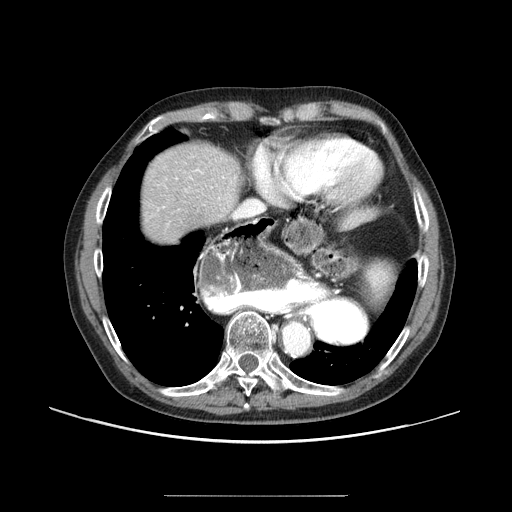
Contrast-enhanced abdominal CT (liver protocol), one axial slice. Position 77 of 91 along the scan axis. Reconstruction kernel STANDARD. 100 kVp. One of 2 acquisitions stored at this slice position. Soft-tissue window (W 400 / L 40 HU). 2.5 mm slice thickness. 512 × 512 image matrix, field of view 400 × 400 mm. From the clinical record (not read from this slice): diagnosis: hepatocellular carcinoma (patient treated with transarterial chemoembolisation; whether this scan precedes or follows treatment is not stated here); TNM stage (as recorded): Stage-I; Child-Pugh class: A; tumour differentiation: moderately differentiated.
Outlined on this slice (semi-automatic segmentation, software-assisted and operator-edited):
- abdominal aorta: bounding box [x1, y1, x2, y2] px = [283, 323, 308, 354]
- liver parenchyma outside the tumour (the mass and vessels are separate outlines, so this box may not span the whole liver): [142, 142, 240, 242]
- liver vessels: [197, 170, 224, 178]